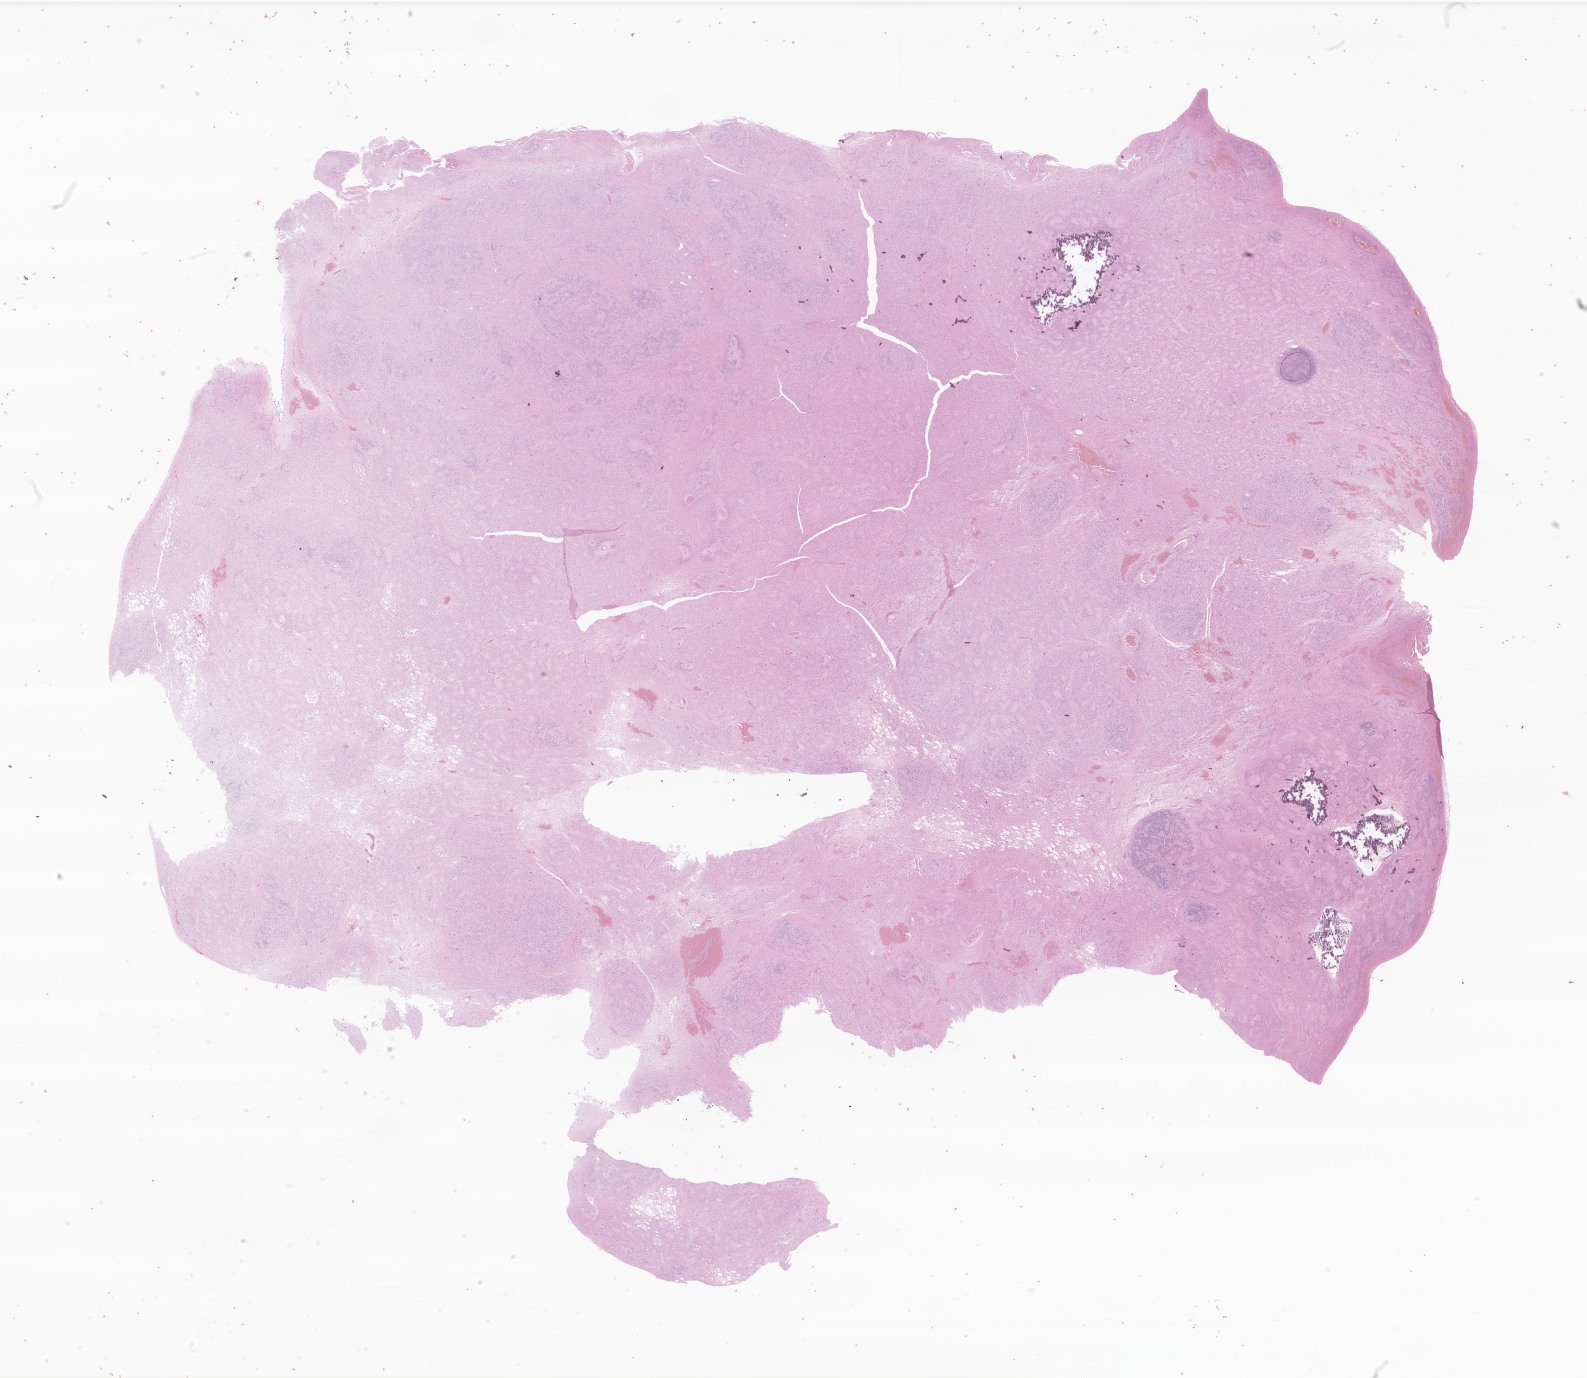
Whole-slide image, H&E stain of tumor tissue from the brain — low-resolution overview of the scanned area, about 26.8 x 23.2 mm, formalin-fixed, paraffin-embedded (FFPE) tissue. Patient: male, age 43 months (3 years 7 months).
* diagnosis: Ependymoma, NOS